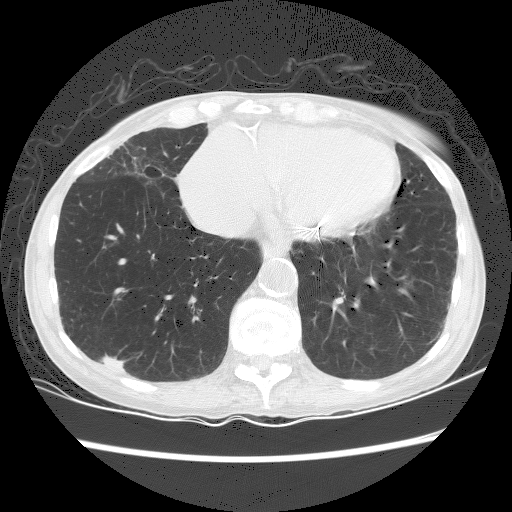
Low-dose screening chest CT, one axial slice; position 59 of 156 along the scan axis; reconstruction kernel BONE; 120 kVp; lung window (W 1500 / L -600 HU); 512 × 512 image matrix, field of view 320 × 320 mm.
Structures marked on this image (outlined manually by an expert reader):
- lesion 1 (tumor, lower lobe of right lung): bounding box <102,354,126,372> (left, top, right, bottom; pixels)